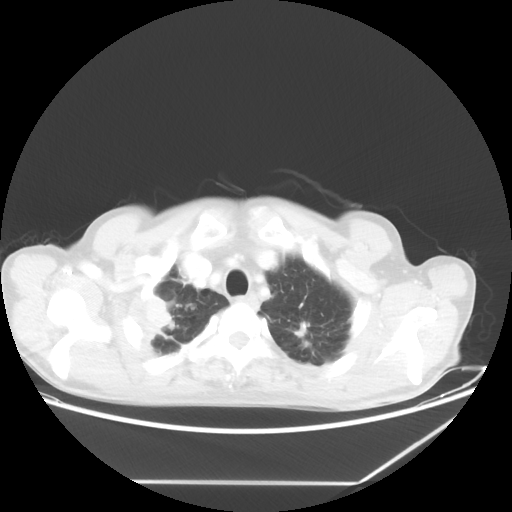
Chest CT, one axial slice; slice 57 of 65 in the series (ordered by position); reconstruction kernel STANDARD; 80 kVp; lung window (W 1500 / L -600 HU); 5 mm slice thickness; 512 × 512 image matrix. Male patient, age 68 years. Case-level facts recorded for this patient, not image findings: clinical TNM (as recorded): T3 N3 M0.
Structures marked on this image (bounding box drawn by a radiologist):
- lung tumour (recorded histology: adenocarcinoma): box from (x=137, y=283) to (x=185, y=352) px